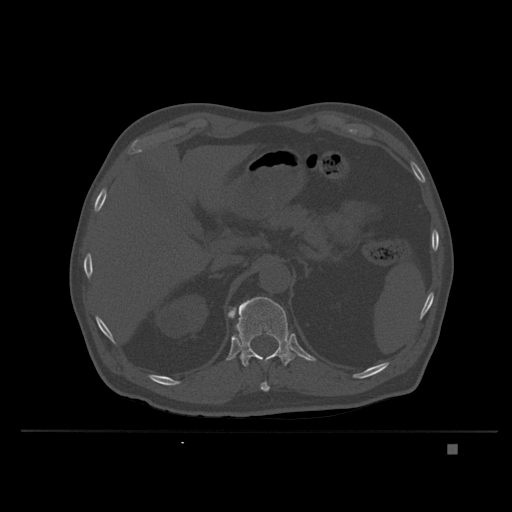
CT including the spine, one axial slice. Position 162 of 435 along the scan axis. Bone window (W 1800 / L 400 HU). 512 × 512 image matrix, field of view 434 × 434 mm. Patient: male, 73 years. From the clinical record (not read from this slice): primary cancer: skin.
Outlined on this slice (semi-automatic segmentation, software-assisted and operator-edited):
- T11 vertebra: bounding box <260,381,270,392> (left, top, right, bottom; pixels)
- T12 vertebra: <228,297,295,367>